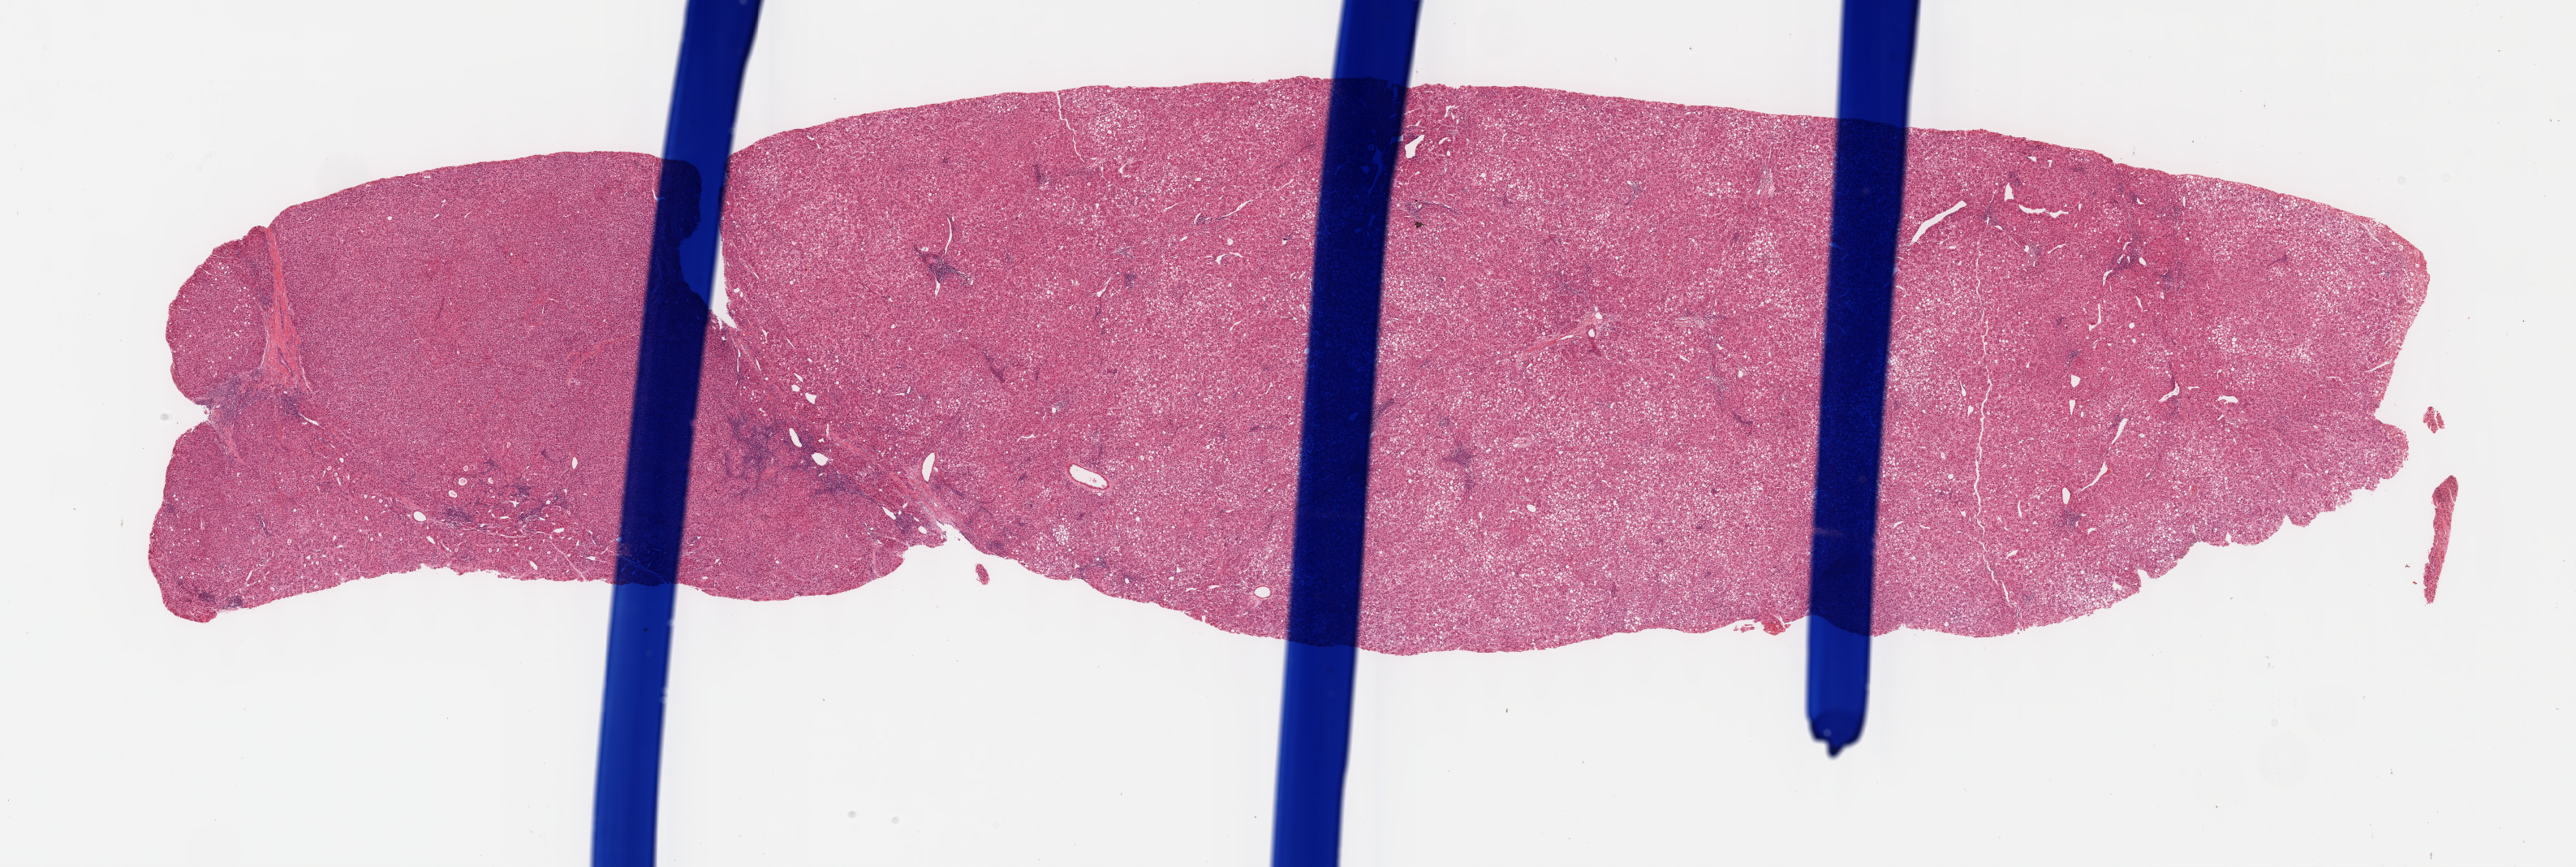
Whole-slide histology image, H&E, whole scanned area (about 25.7 x 8.6 mm, from a 40x scan) shown as a low-resolution overview. FFPE section. Sample: primary tumour, liver. Patient: male, age at initial diagnosis 51 years. Histologic grade: G3 (poorly differentiated).
* TNM: T2 N0 M0
* AJCC pathologic stage: II (7th edition)
* histologic diagnosis: Hepatocellular carcinoma, NOS